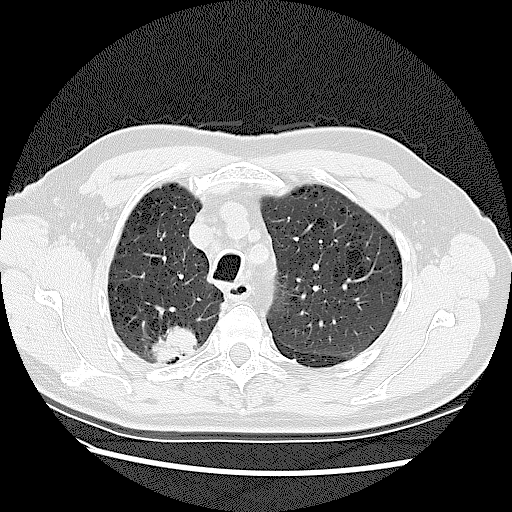
Low-dose screening chest CT, one axial slice. Position 98 of 128 along the scan axis. Lung window (W 1500 / L -600 HU). 2.5 mm slice thickness. 512 × 512 image matrix.
Annotated regions visible in this slice (manually delineated by an expert):
- lesion 2 (tumor, upper lobe of right lung): bounding box <152,328,197,364> (left, top, right, bottom; pixels)